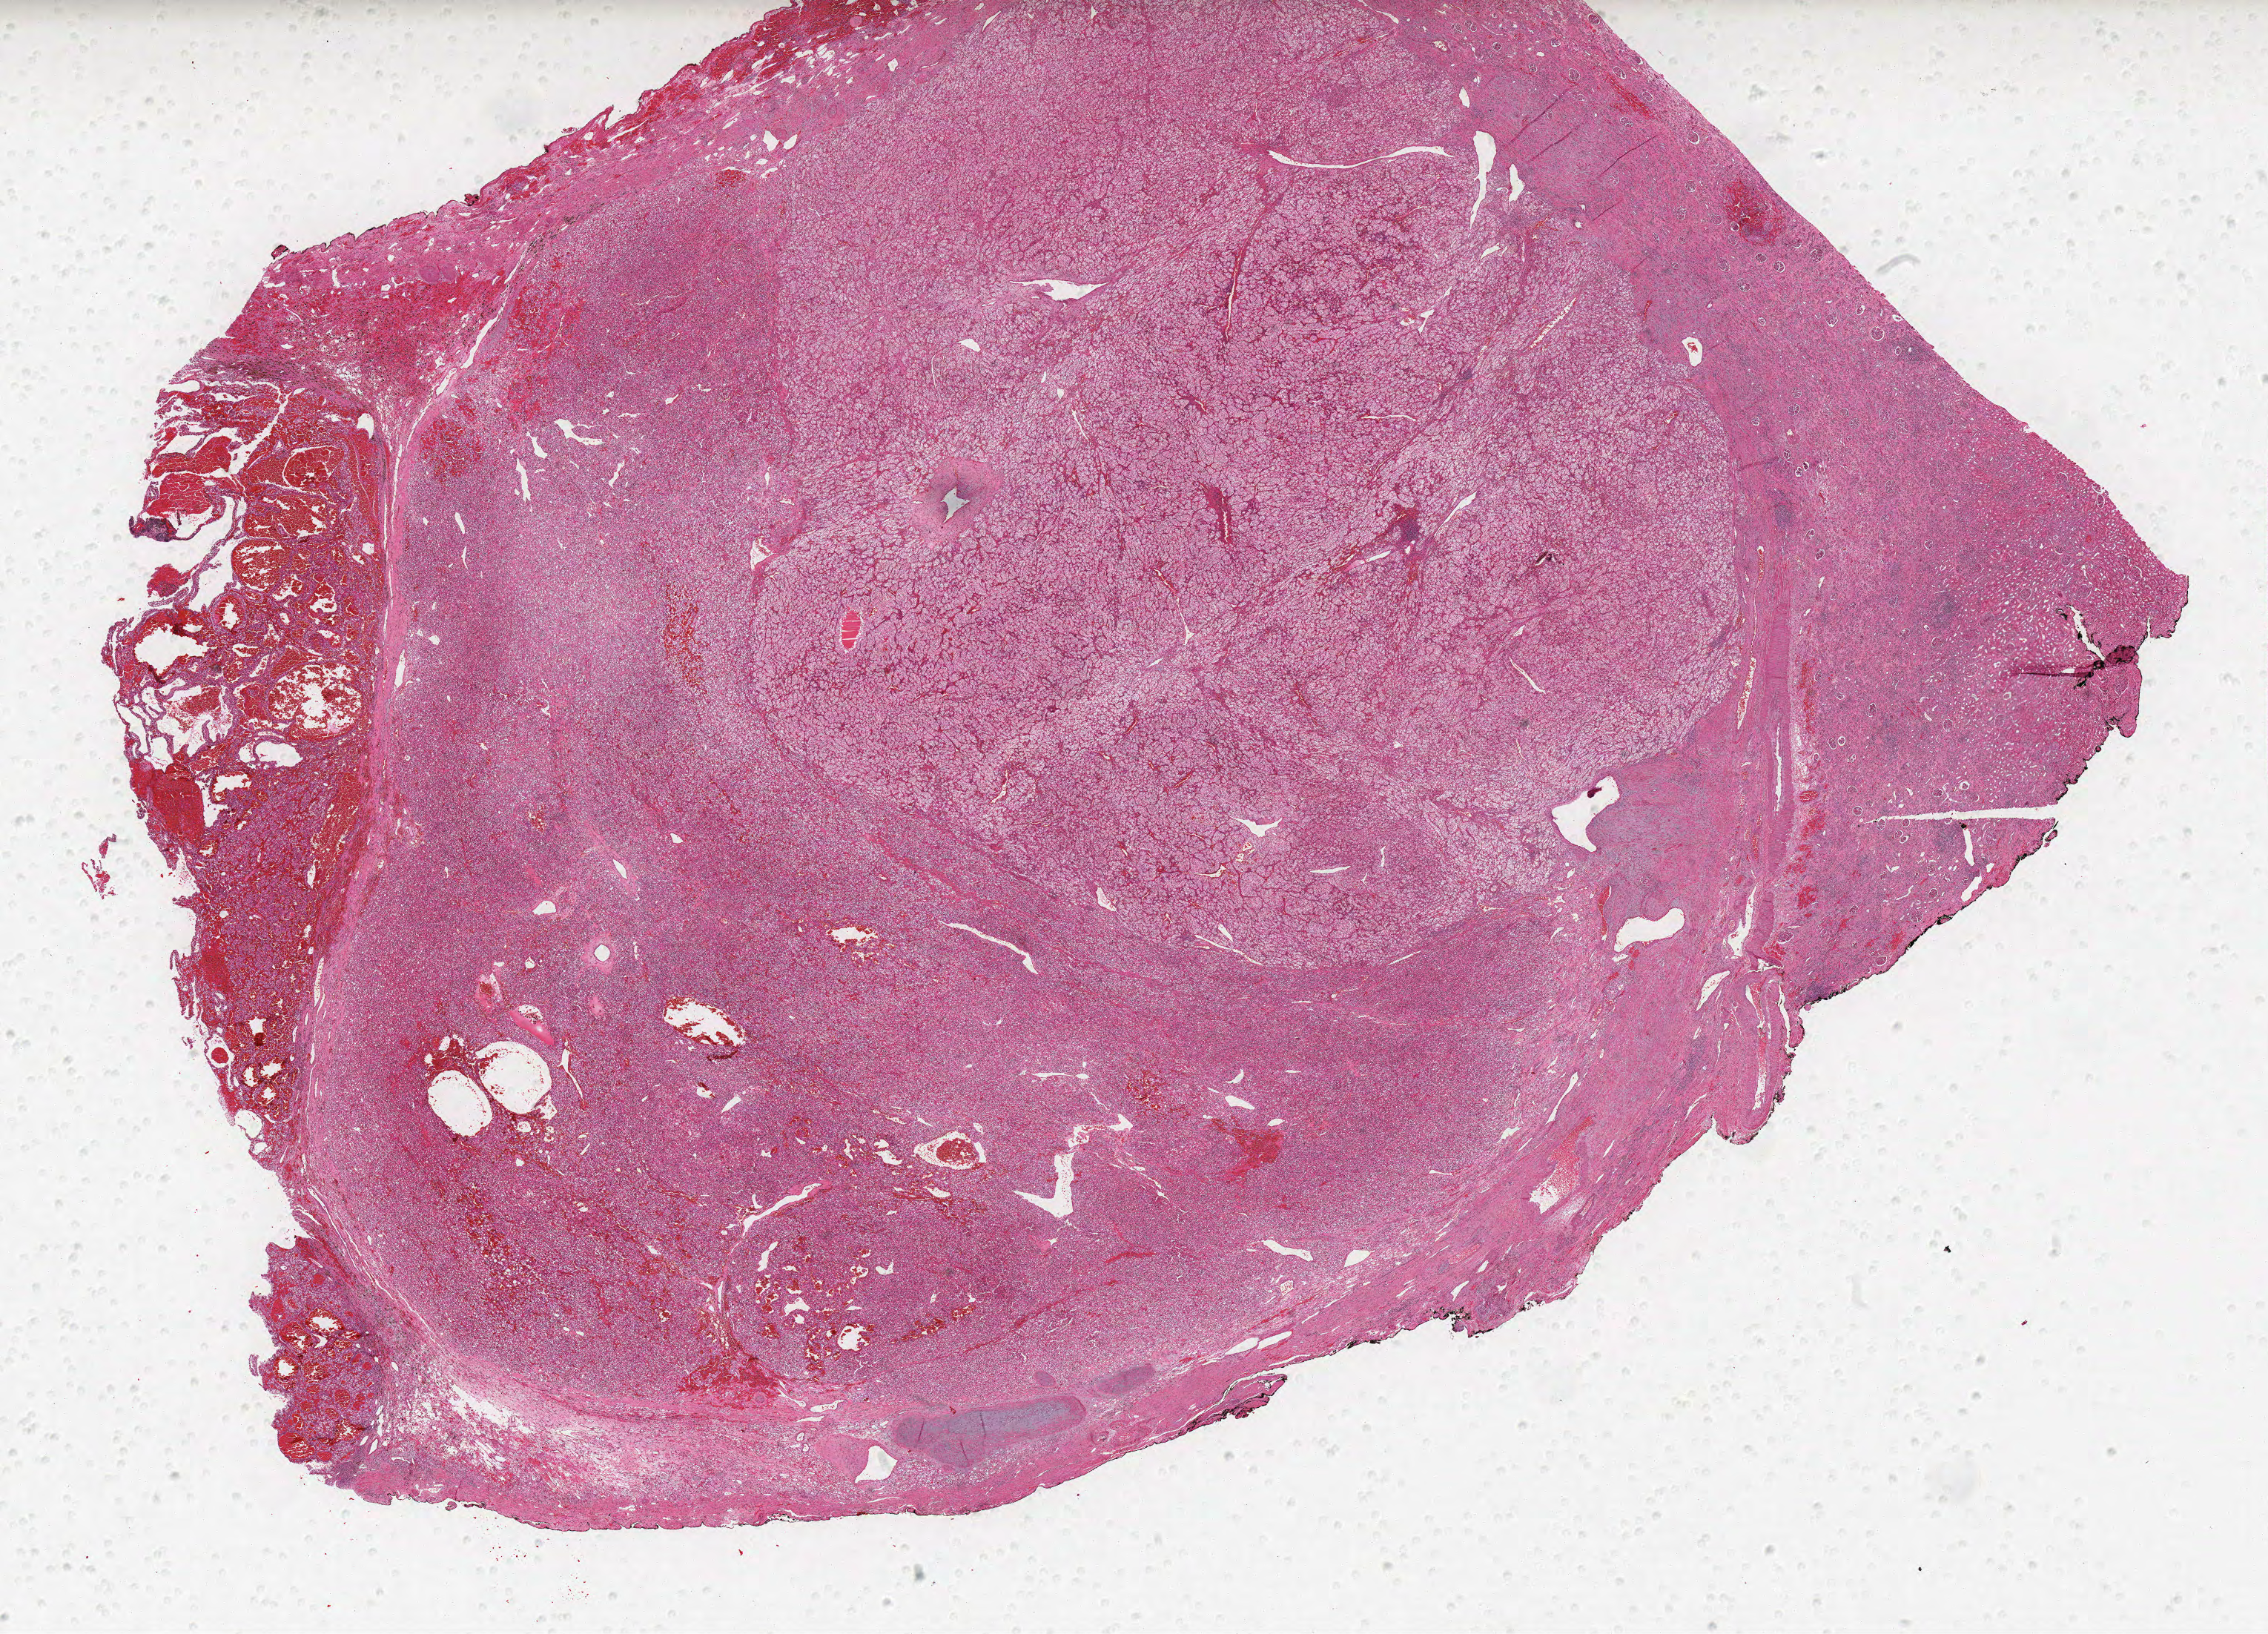
H&E whole-slide image, a low-resolution overview of the entire scanned area, about 24.5 x 17.6 mm, formalin-fixed paraffin-embedded (FFPE) diagnostic section, sample: primary tumour, kidney. Patient: male, age at initial diagnosis 53 years. Histologic grade: G3 (poorly differentiated).
Histologic diagnosis: Clear cell adenocarcinoma, NOS. AJCC pathologic stage: I.